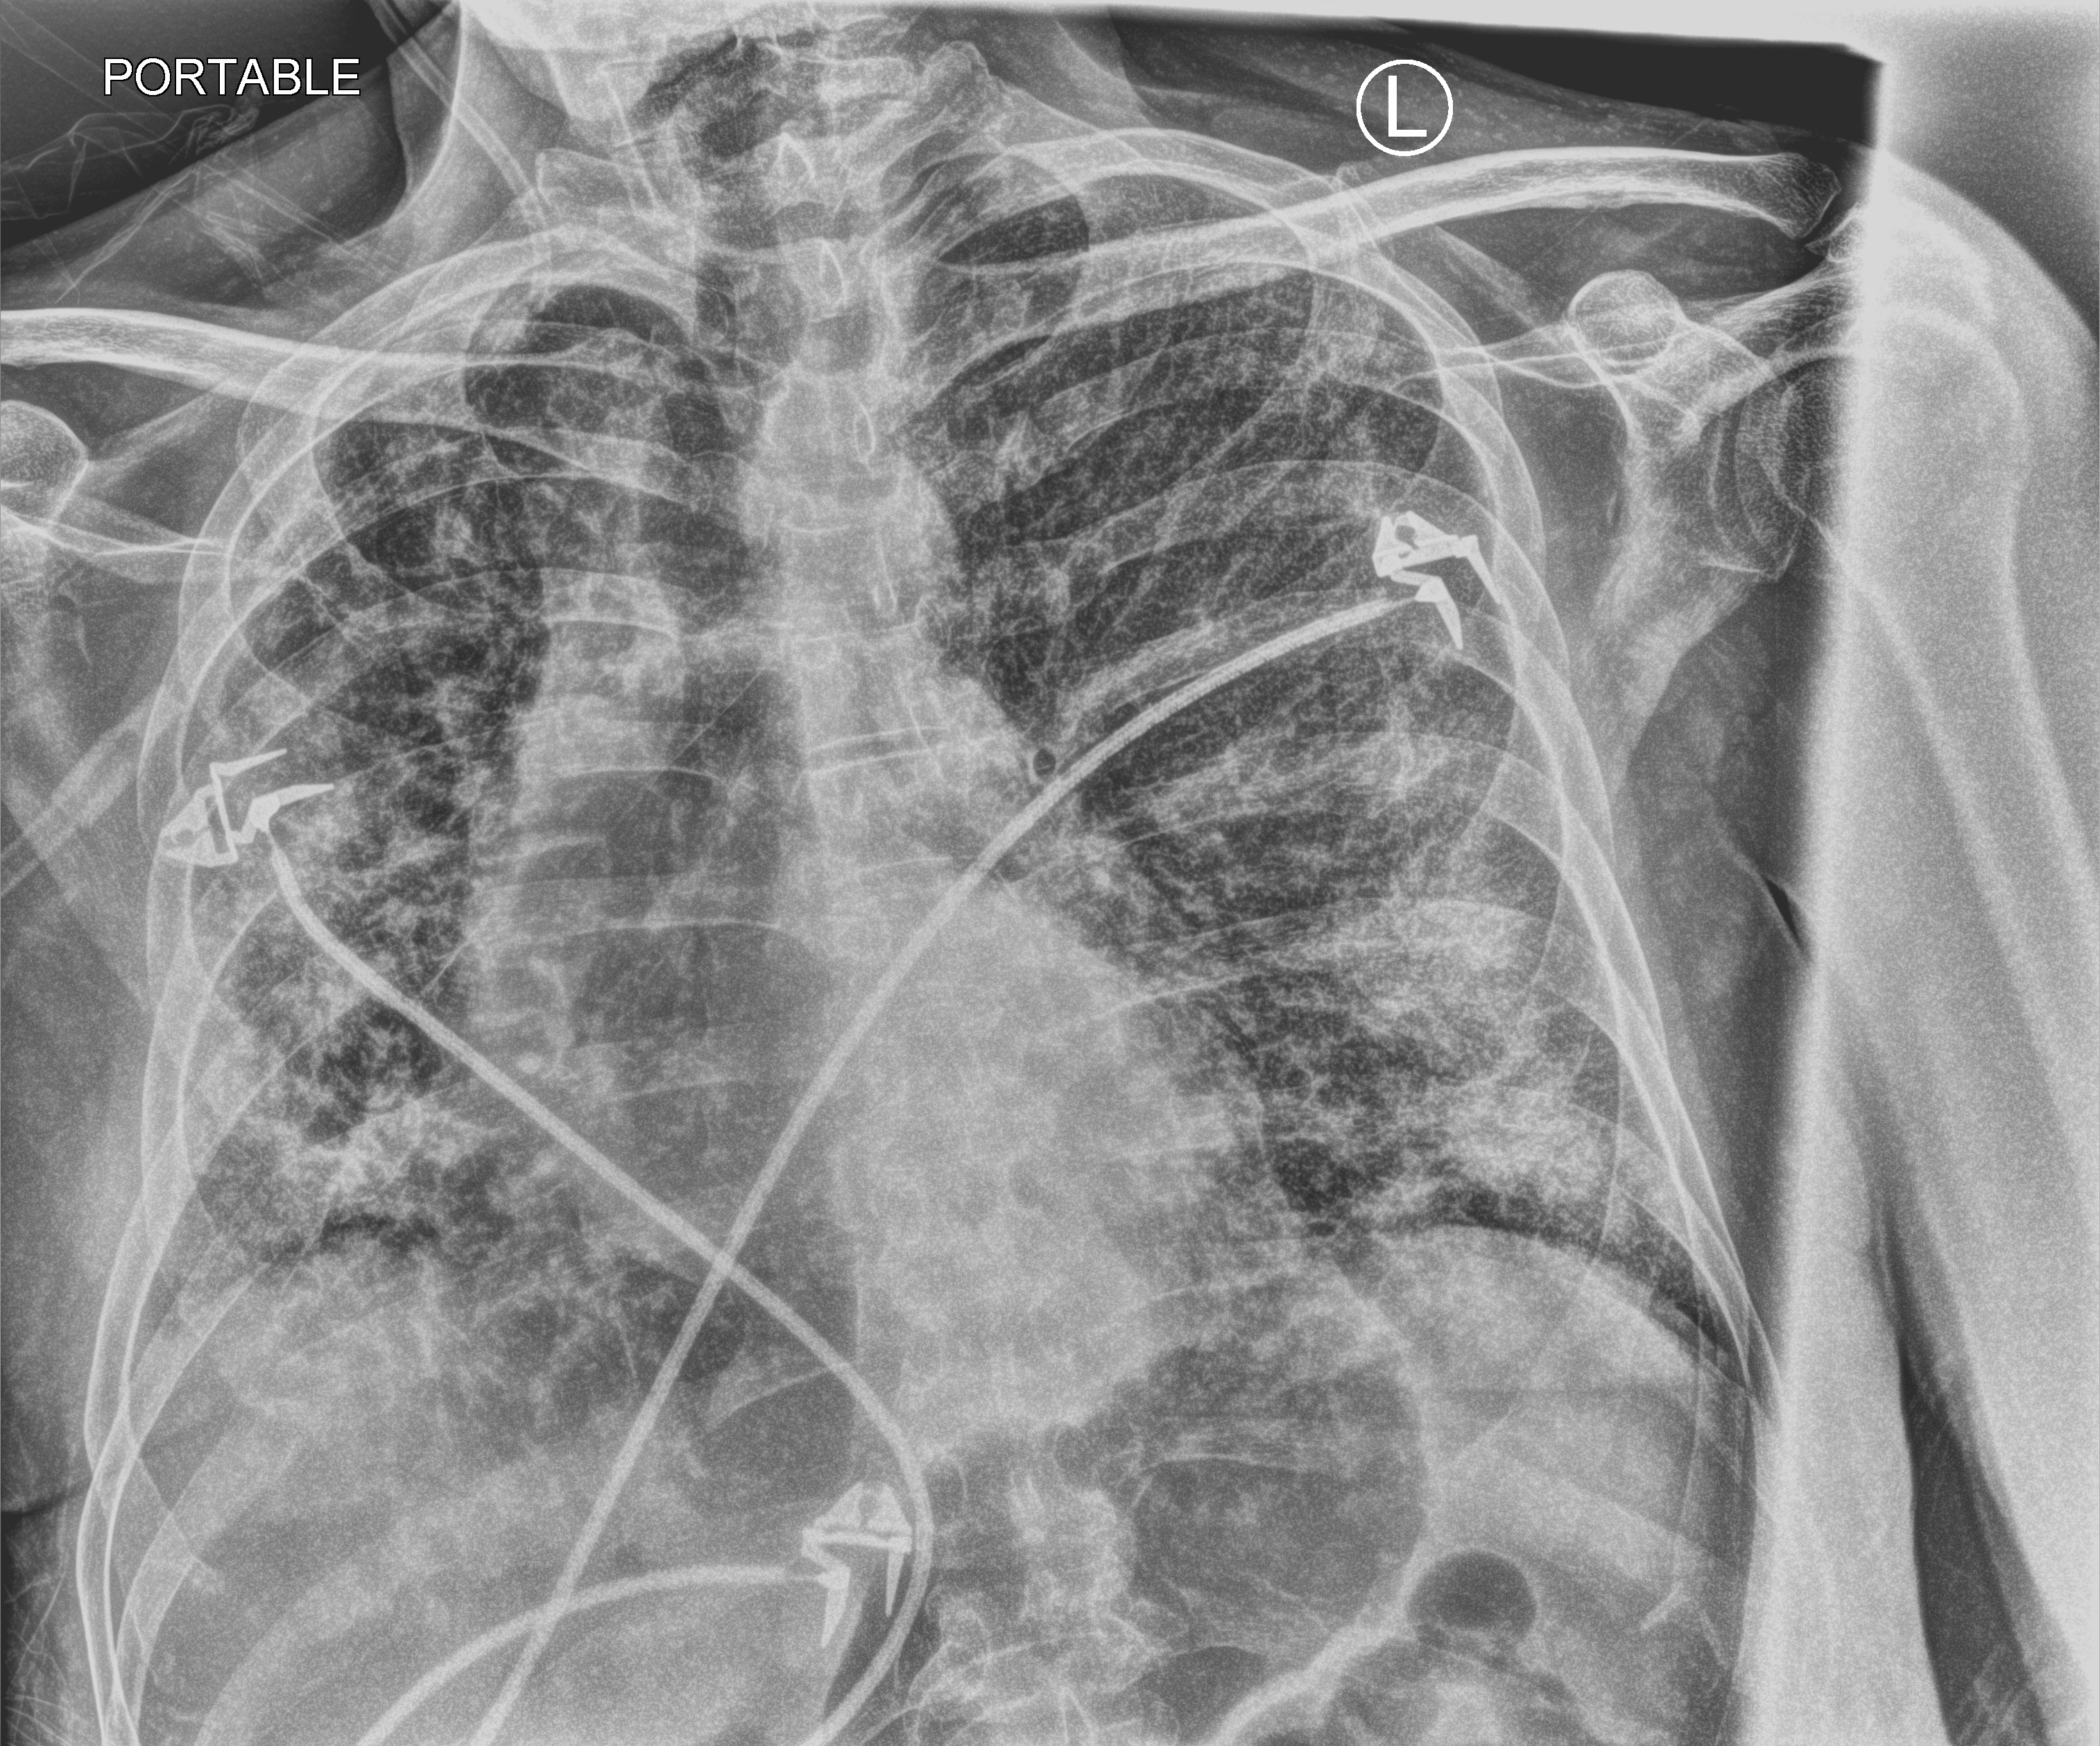
Portable chest radiograph; anteroposterior (AP) projection. Patient hospitalised with COVID-19; male, aged 60–74 years.
Hospital-stay facts (about this admission, not read from this image; timing relative to this image not recorded):
- mechanically ventilated during this hospital stay: no